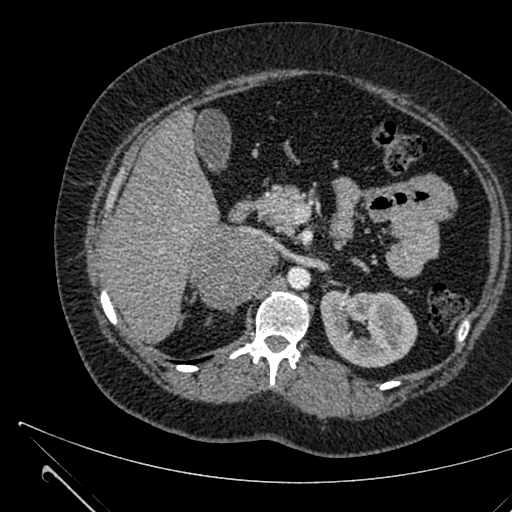
Contrast-enhanced abdominal CT, one axial slice. Position 397 of 731 along the scan axis. Intravenous contrast given. Soft-tissue window (W 400 / L 40 HU). 1 mm slice thickness. 512 × 512 image matrix, field of view 376 × 376 mm. Patient: female, 36 years. Case-level facts recorded for this patient, not image findings: diagnosis: adrenocortical carcinoma; tumour side: right adrenal; tumour size at pathology: 10 cm; Ki-67 index: 20 %; stage (as recorded): 4.
Annotated regions visible in this slice (semi-automatically segmented with operator editing):
- mass: bounding box (x1, y1, x2, y2) in pixels: (194, 232, 272, 308)